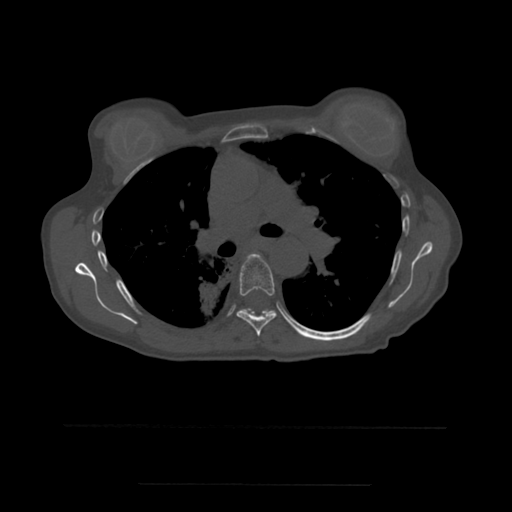
CT including the spine, one axial slice. Slice 374 of 544 in the series (ordered by position). Bone window (W 1800 / L 400 HU). 512 × 512 image matrix. Patient age 58 years. From the clinical record (not read from this slice): primary cancer: lung.
Structures marked on this image (semi-automatically segmented with operator editing):
- T6 vertebra: bounding box (x1, y1, x2, y2) in pixels: (236, 254, 277, 337)
- T7 vertebra: (241, 309, 269, 311)